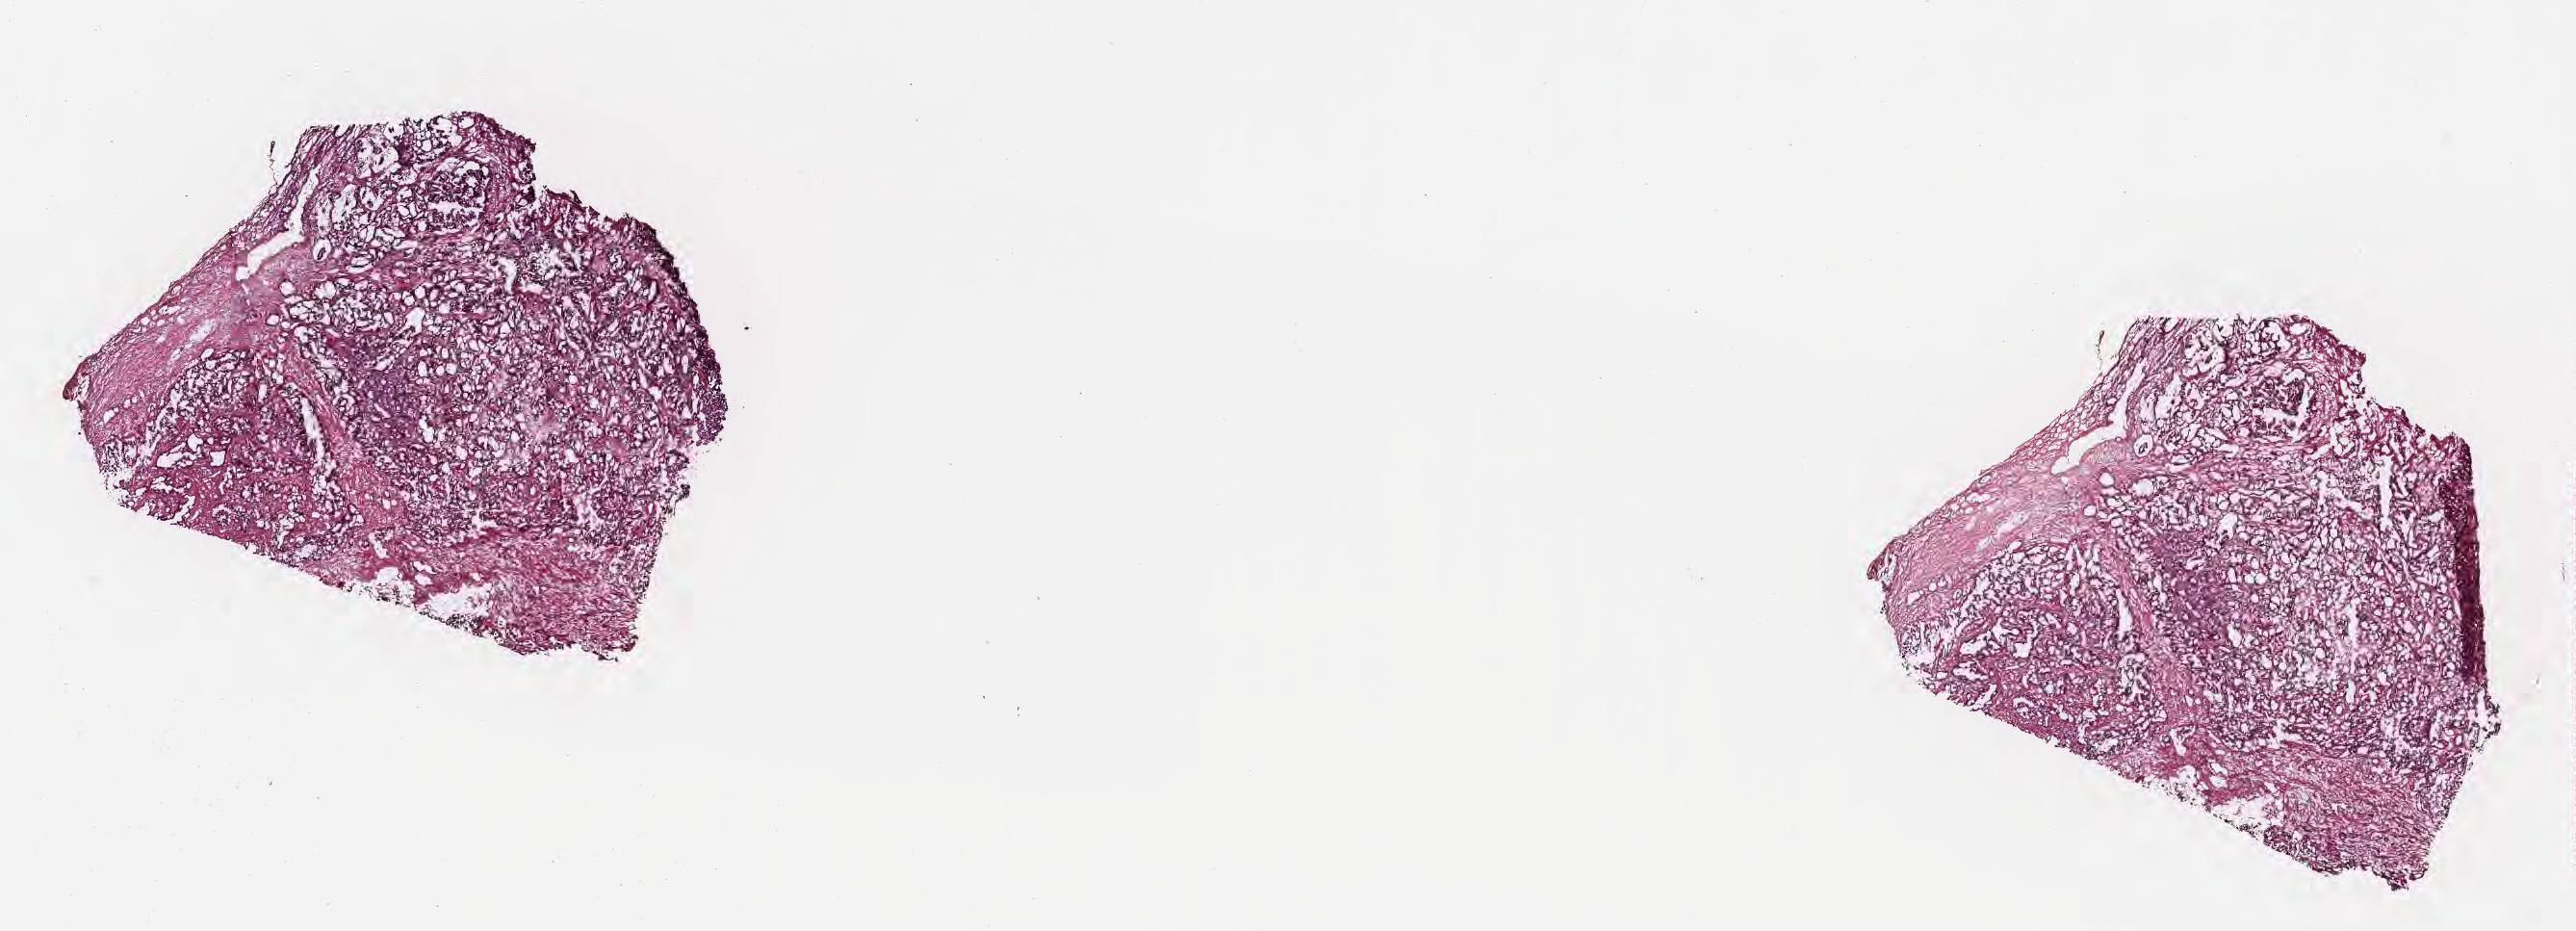
Whole-slide image, hematoxylin and eosin (H&E) stain, a low-resolution overview of the entire scanned area, about 21.6 x 7.8 mm; cryosection; metastatic tumor tissue, resected from lymph node. Male patient; age at initial diagnosis 72 years. Slide review estimates, as recorded: tumor cells 40%, tumor nuclei 40%, stromal cells 20%, necrosis 0%, normal cells 40%. Infiltration values recorded for this section: lymphocyte infiltration 8%, monocyte infiltration 1%, neutrophil infiltration 4%.
- patient diagnosis (primary): Intraductal papillary mucinous neoplasm with invasive carcinoma